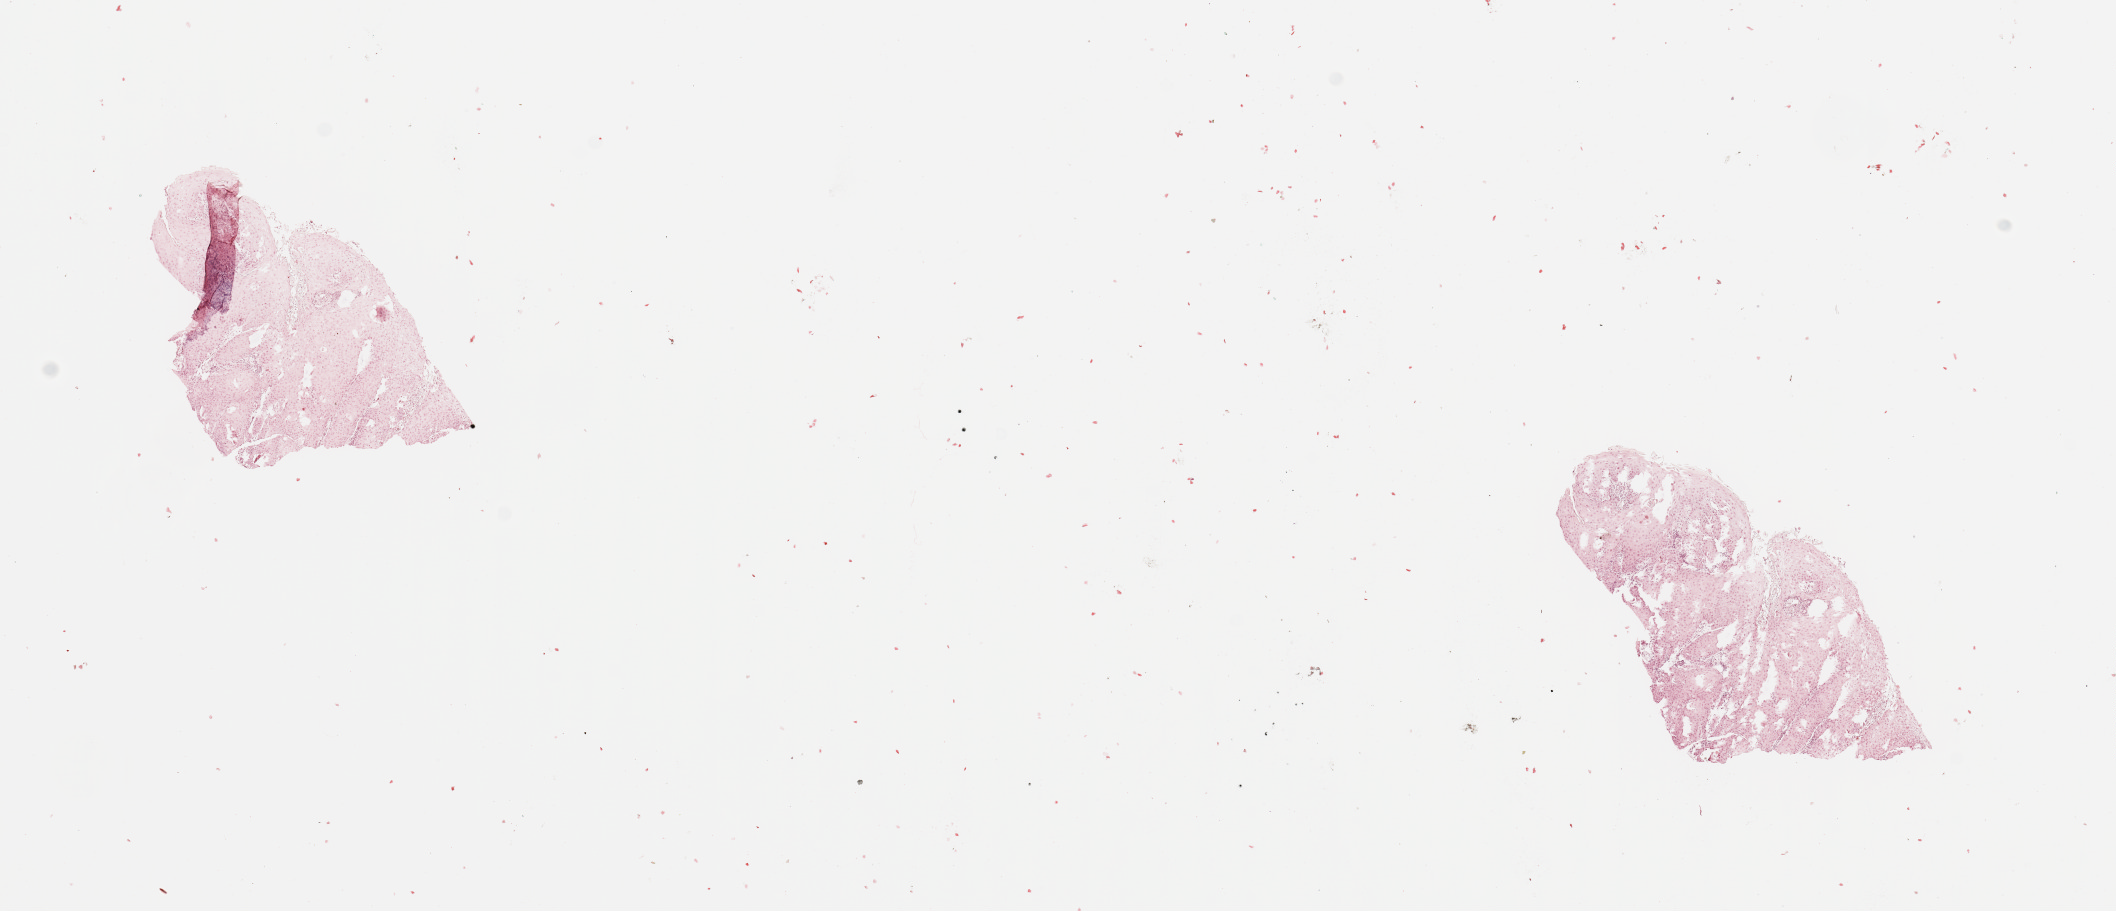
Digitized Hematoxylin and eosin (H&E) stained tissue section (whole slide), low-resolution overview of the scanned area, about 16.7 x 7.2 mm. Tumour tissue sample, sampled site: larynx. Patient: male, age 68 years. Histologic grade: G2 (moderately differentiated). Composition of this section per pathologist review: tumour nuclei 90%, necrosis 0%.
Primary tumour site (as recorded): larynx. Diagnosis: Squamous cell carcinoma, NOS (larynx, NOS). AJCC pathologic stage: III.